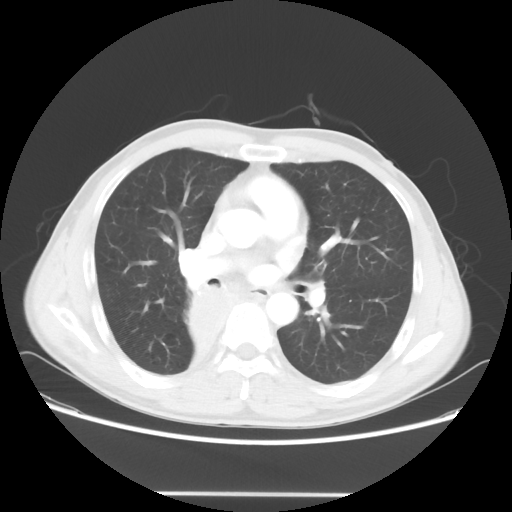
Chest CT, one axial slice; slice 34 of 62 in the series (ordered by position); reconstruction kernel STANDARD; lung window (W 1500 / L -600 HU); 5 mm slice thickness; 512 × 512 image matrix, field of view 393 × 393 mm. Patient: male, 47 years. Case-level facts recorded for this patient, not image findings: clinical TNM (as recorded): T2 N0 M0.
Structures marked on this image (bounding box drawn by a radiologist):
- lung tumour (recorded histology: squamous cell carcinoma): box from (x=175, y=270) to (x=237, y=381) px